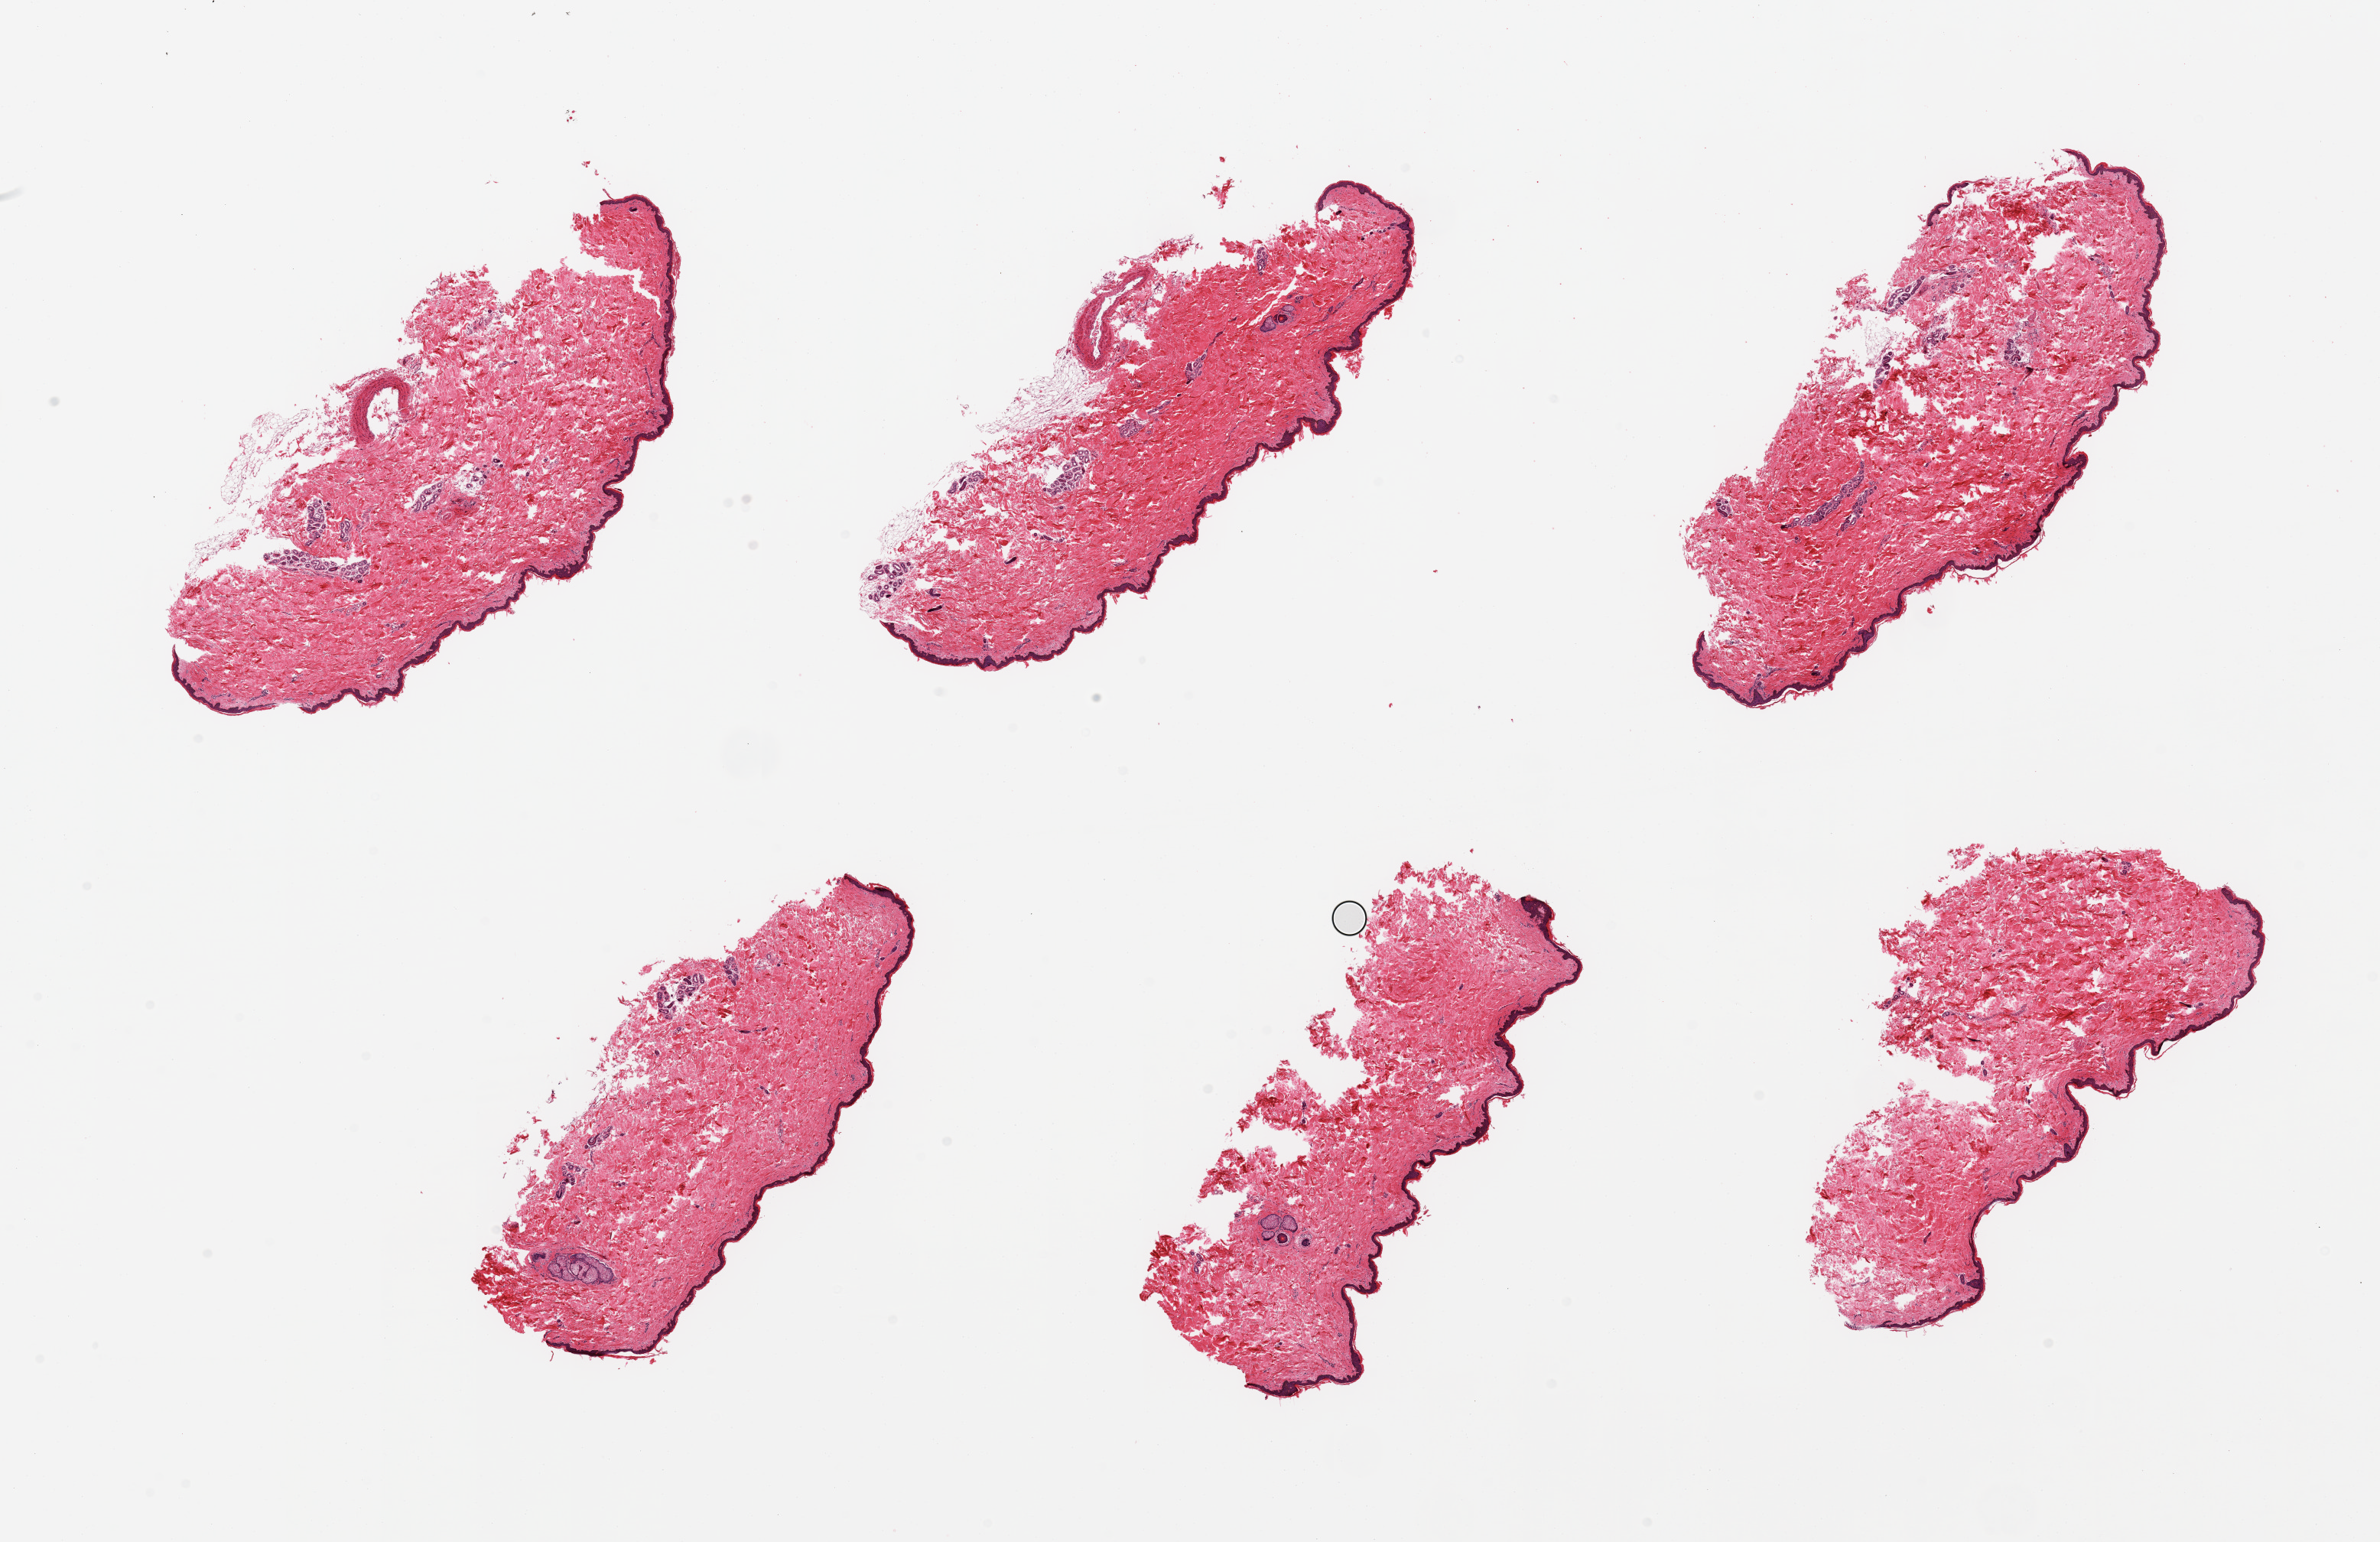
Hematoxylin and eosin (H&E) whole-slide image, brightfield, shown as a low-resolution overview of the whole scanned area (about 24.6 x 15.9 mm, from a 20x scan). PAXgene-fixed, paraffin-embedded tissue. Sampled site (target tissue): skin of suprapubic region. Tissue donor sample. Donor: male.
Review note (as recorded): 6 pieces; well trimmed; <5% dermal fat.